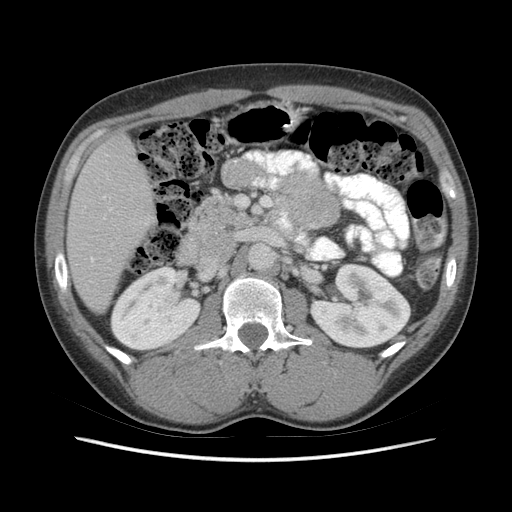
Contrast-enhanced abdominal CT (liver protocol), one axial slice; slice 22 of 73 in the series (ordered by position); 140 kVp; soft-tissue window (W 400 / L 40 HU); 2.5 mm slice thickness; 512 × 512 image matrix, field of view 360 × 360 mm. Case-level facts recorded for this patient, not image findings: diagnosis: hepatocellular carcinoma (patient treated with transarterial chemoembolisation; whether this scan precedes or follows treatment is not stated here); TNM stage (as recorded): Stage-IIIA; Child-Pugh class: A; tumour nodularity: multinodular; tumour size: 6.6 cm.
Outlined on this slice (semi-automatically segmented with operator editing):
- liver parenchyma outside the tumour (the mass and vessels are separate outlines, so this box may not span the whole liver): bounding box [x1, y1, x2, y2] px = [66, 136, 154, 312]
- liver vessels: [91, 208, 112, 262]